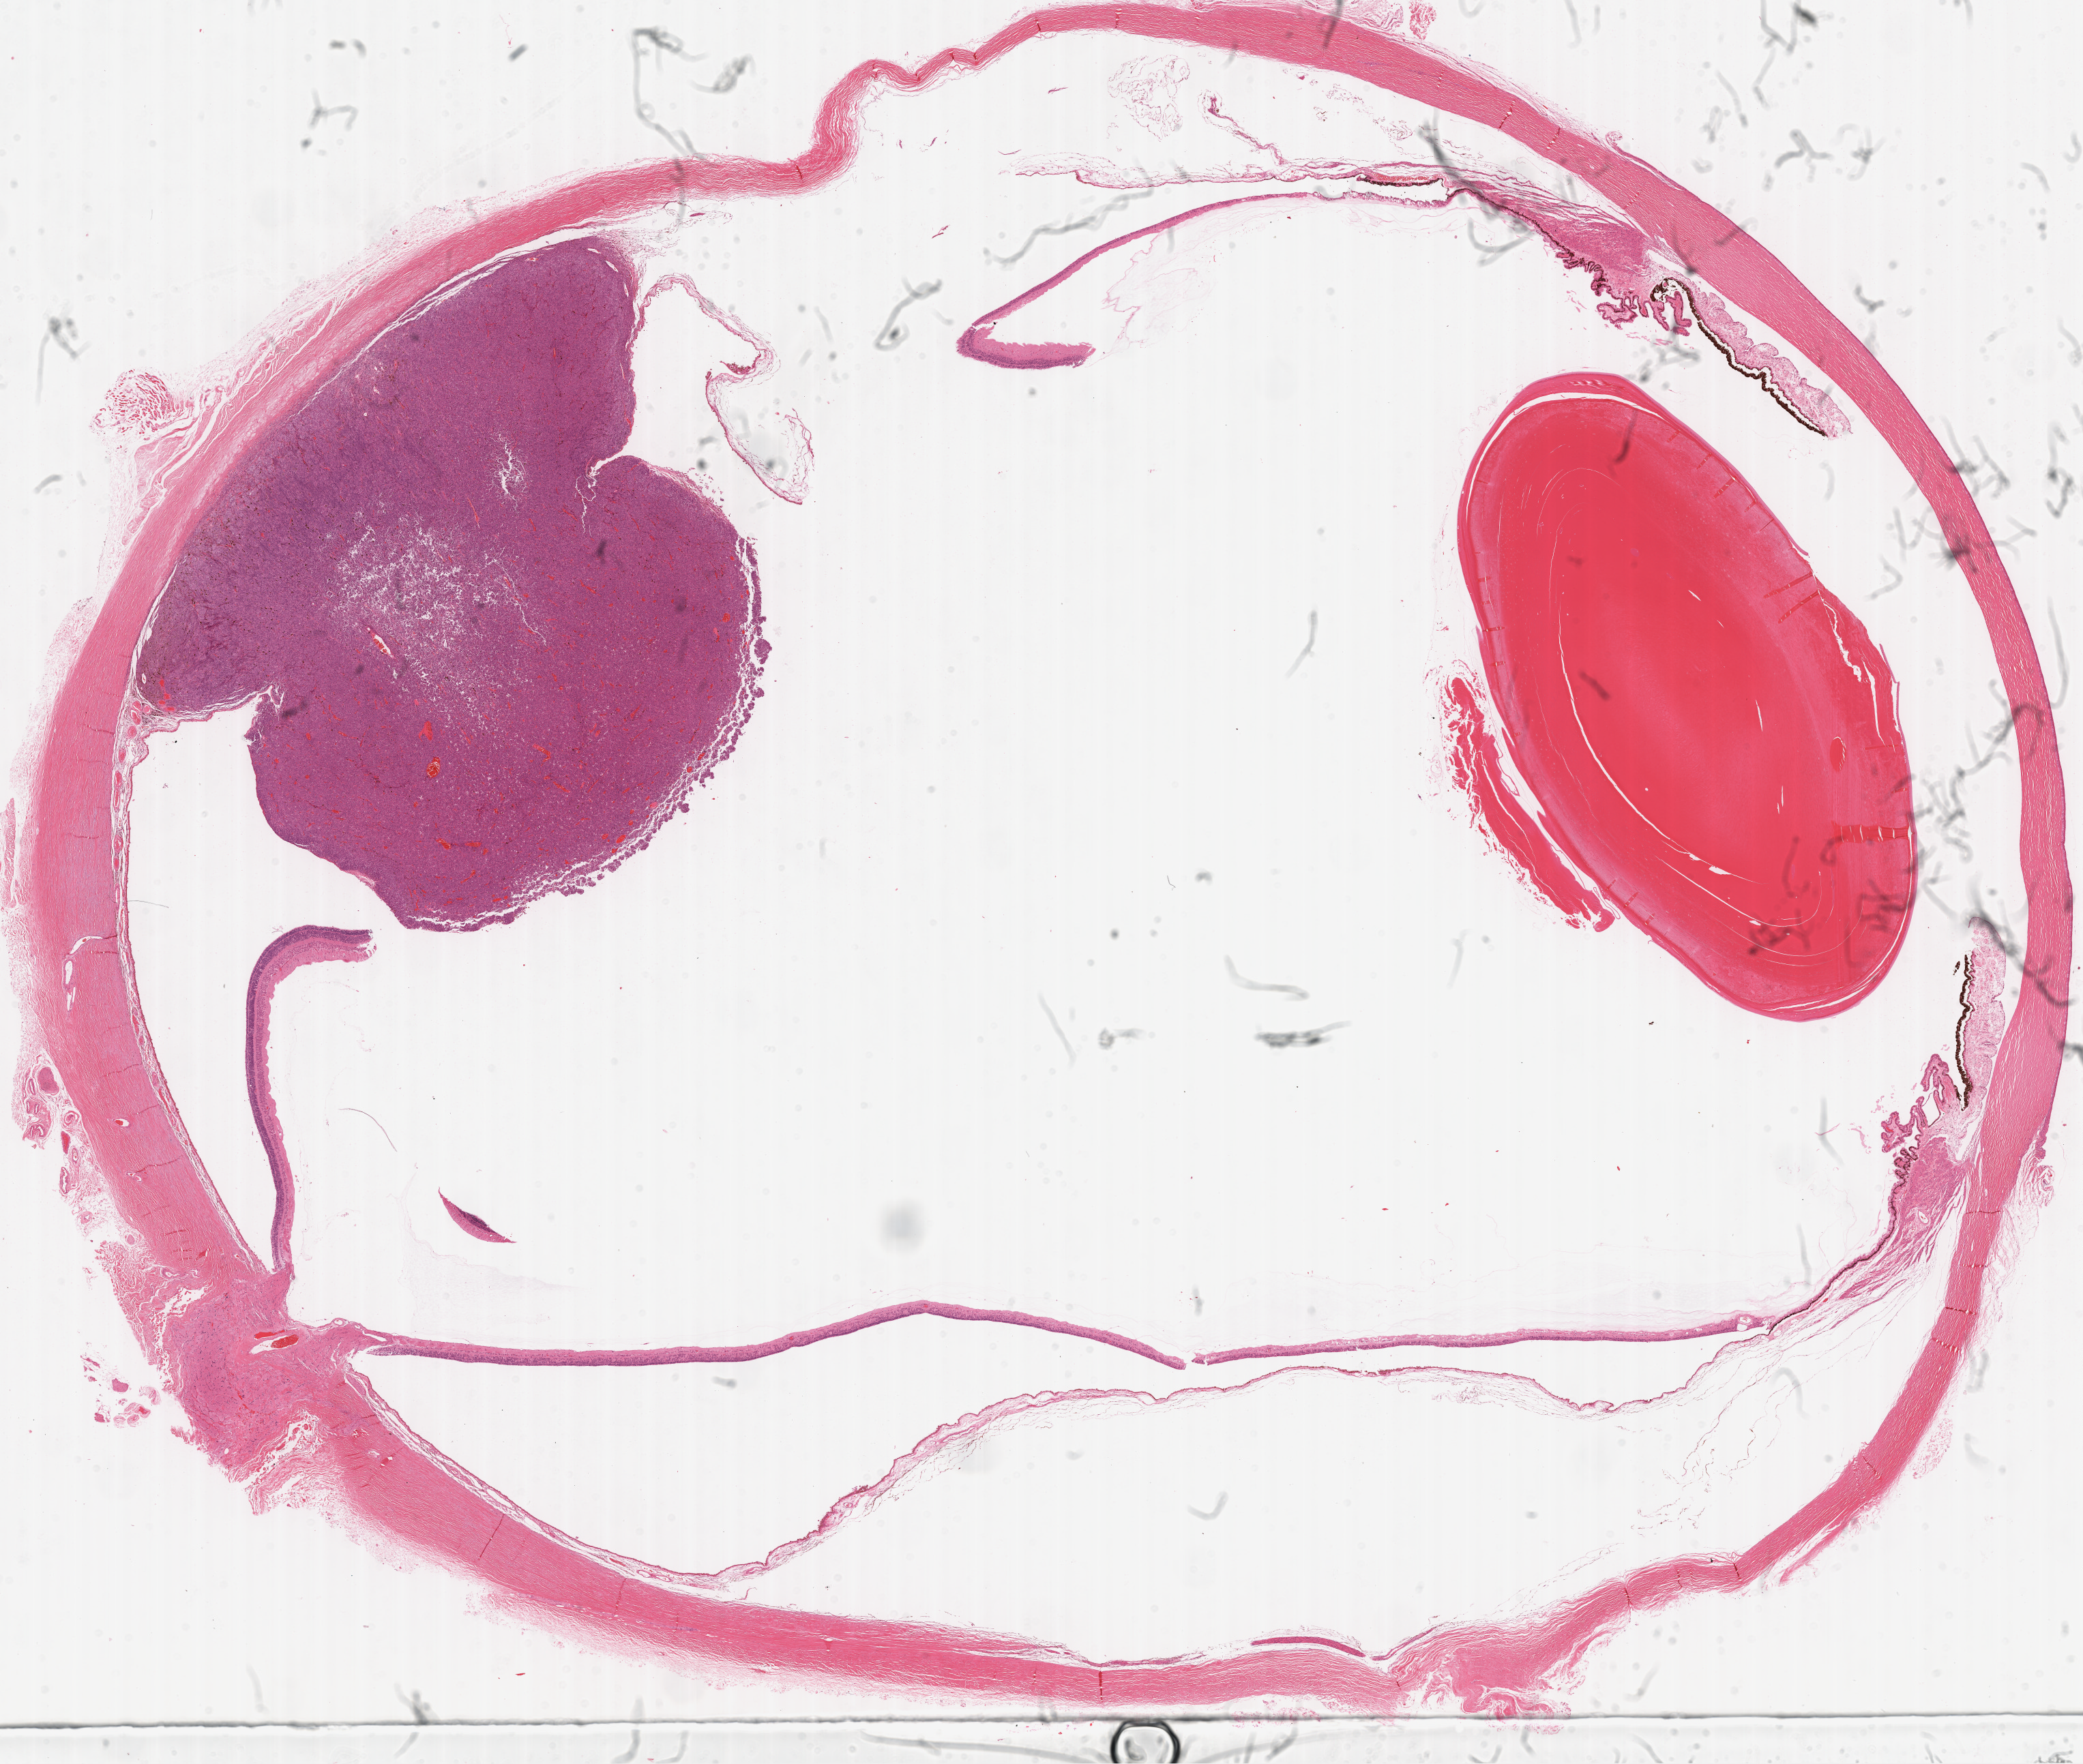
Hematoxylin and eosin (H&E) stained whole-slide image, shown as a low-resolution overview of the whole scanned area (about 24.6 x 20.9 mm); formalin-fixed paraffin-embedded (FFPE) diagnostic section; uvea, primary tumour sample. Female patient; age at initial diagnosis 74 years. Slide review estimates, as recorded: tumour cells 50%, tumour nuclei 60%, normal cells 50%, stromal cells 0%, necrosis 0%. Infiltration values recorded for this section: lymphocyte infiltration 1%, monocyte infiltration 0%, neutrophil infiltration 0%.
Laterality: left. AJCC pathologic stage: IIA (7th edition). Pathologic diagnosis: Mixed epithelioid and spindle cell melanoma (choroid).